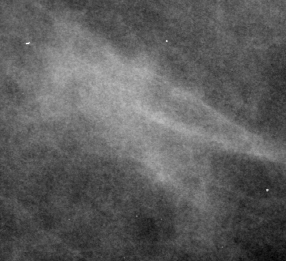
Region of interest cut from a scanned film mammogram (one marked finding); left breast; MLO view; BI-RADS breast density category 1 (scale 1–4).
- Mass, shape irregular, margins ill defined; BI-RADS assessment category 4; subtlety rating 4 on a 1 (subtle) to 5 (obvious) scale; pathology (as recorded): benign.